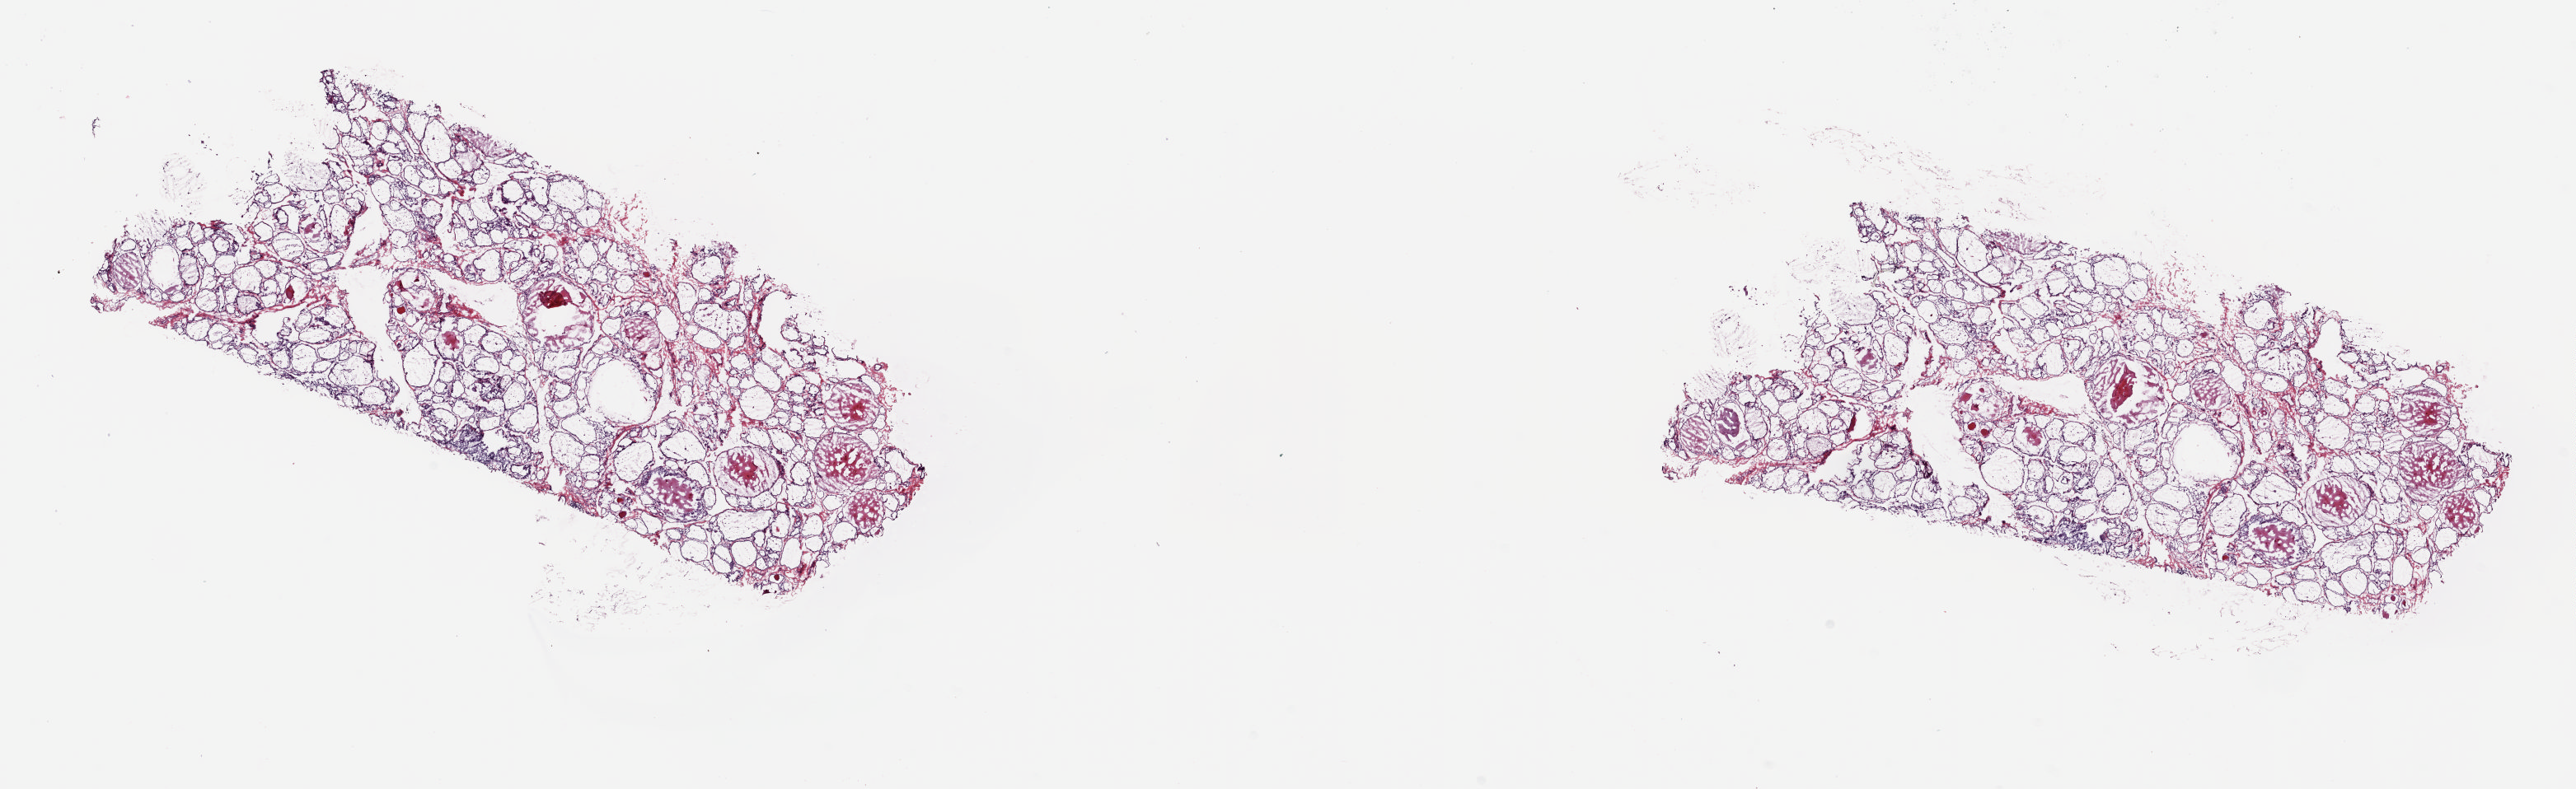
Digitized Hematoxylin and eosin (H&E) stained tissue section (whole slide) — low-resolution overview of the scanned area, about 24.8 x 7.6 mm (from a 20x scan). Frozen section from the top of the tissue portion. Thyroid, solid tissue normal (non-tumour tissue) sample. Female, age 59 years at initial diagnosis. Slide review estimates, as recorded: tumour cells 0%, tumour nuclei 0%, normal cells 100%, stromal cells 0%, necrosis 0%. Inflammatory infiltration, as recorded: lymphocyte infiltration 0%, monocyte infiltration 2%, neutrophil infiltration 0%.
This section: solid tissue normal (non-tumour) sample from the same patient. Patient diagnosis: Papillary adenocarcinoma, NOS (thyroid gland).